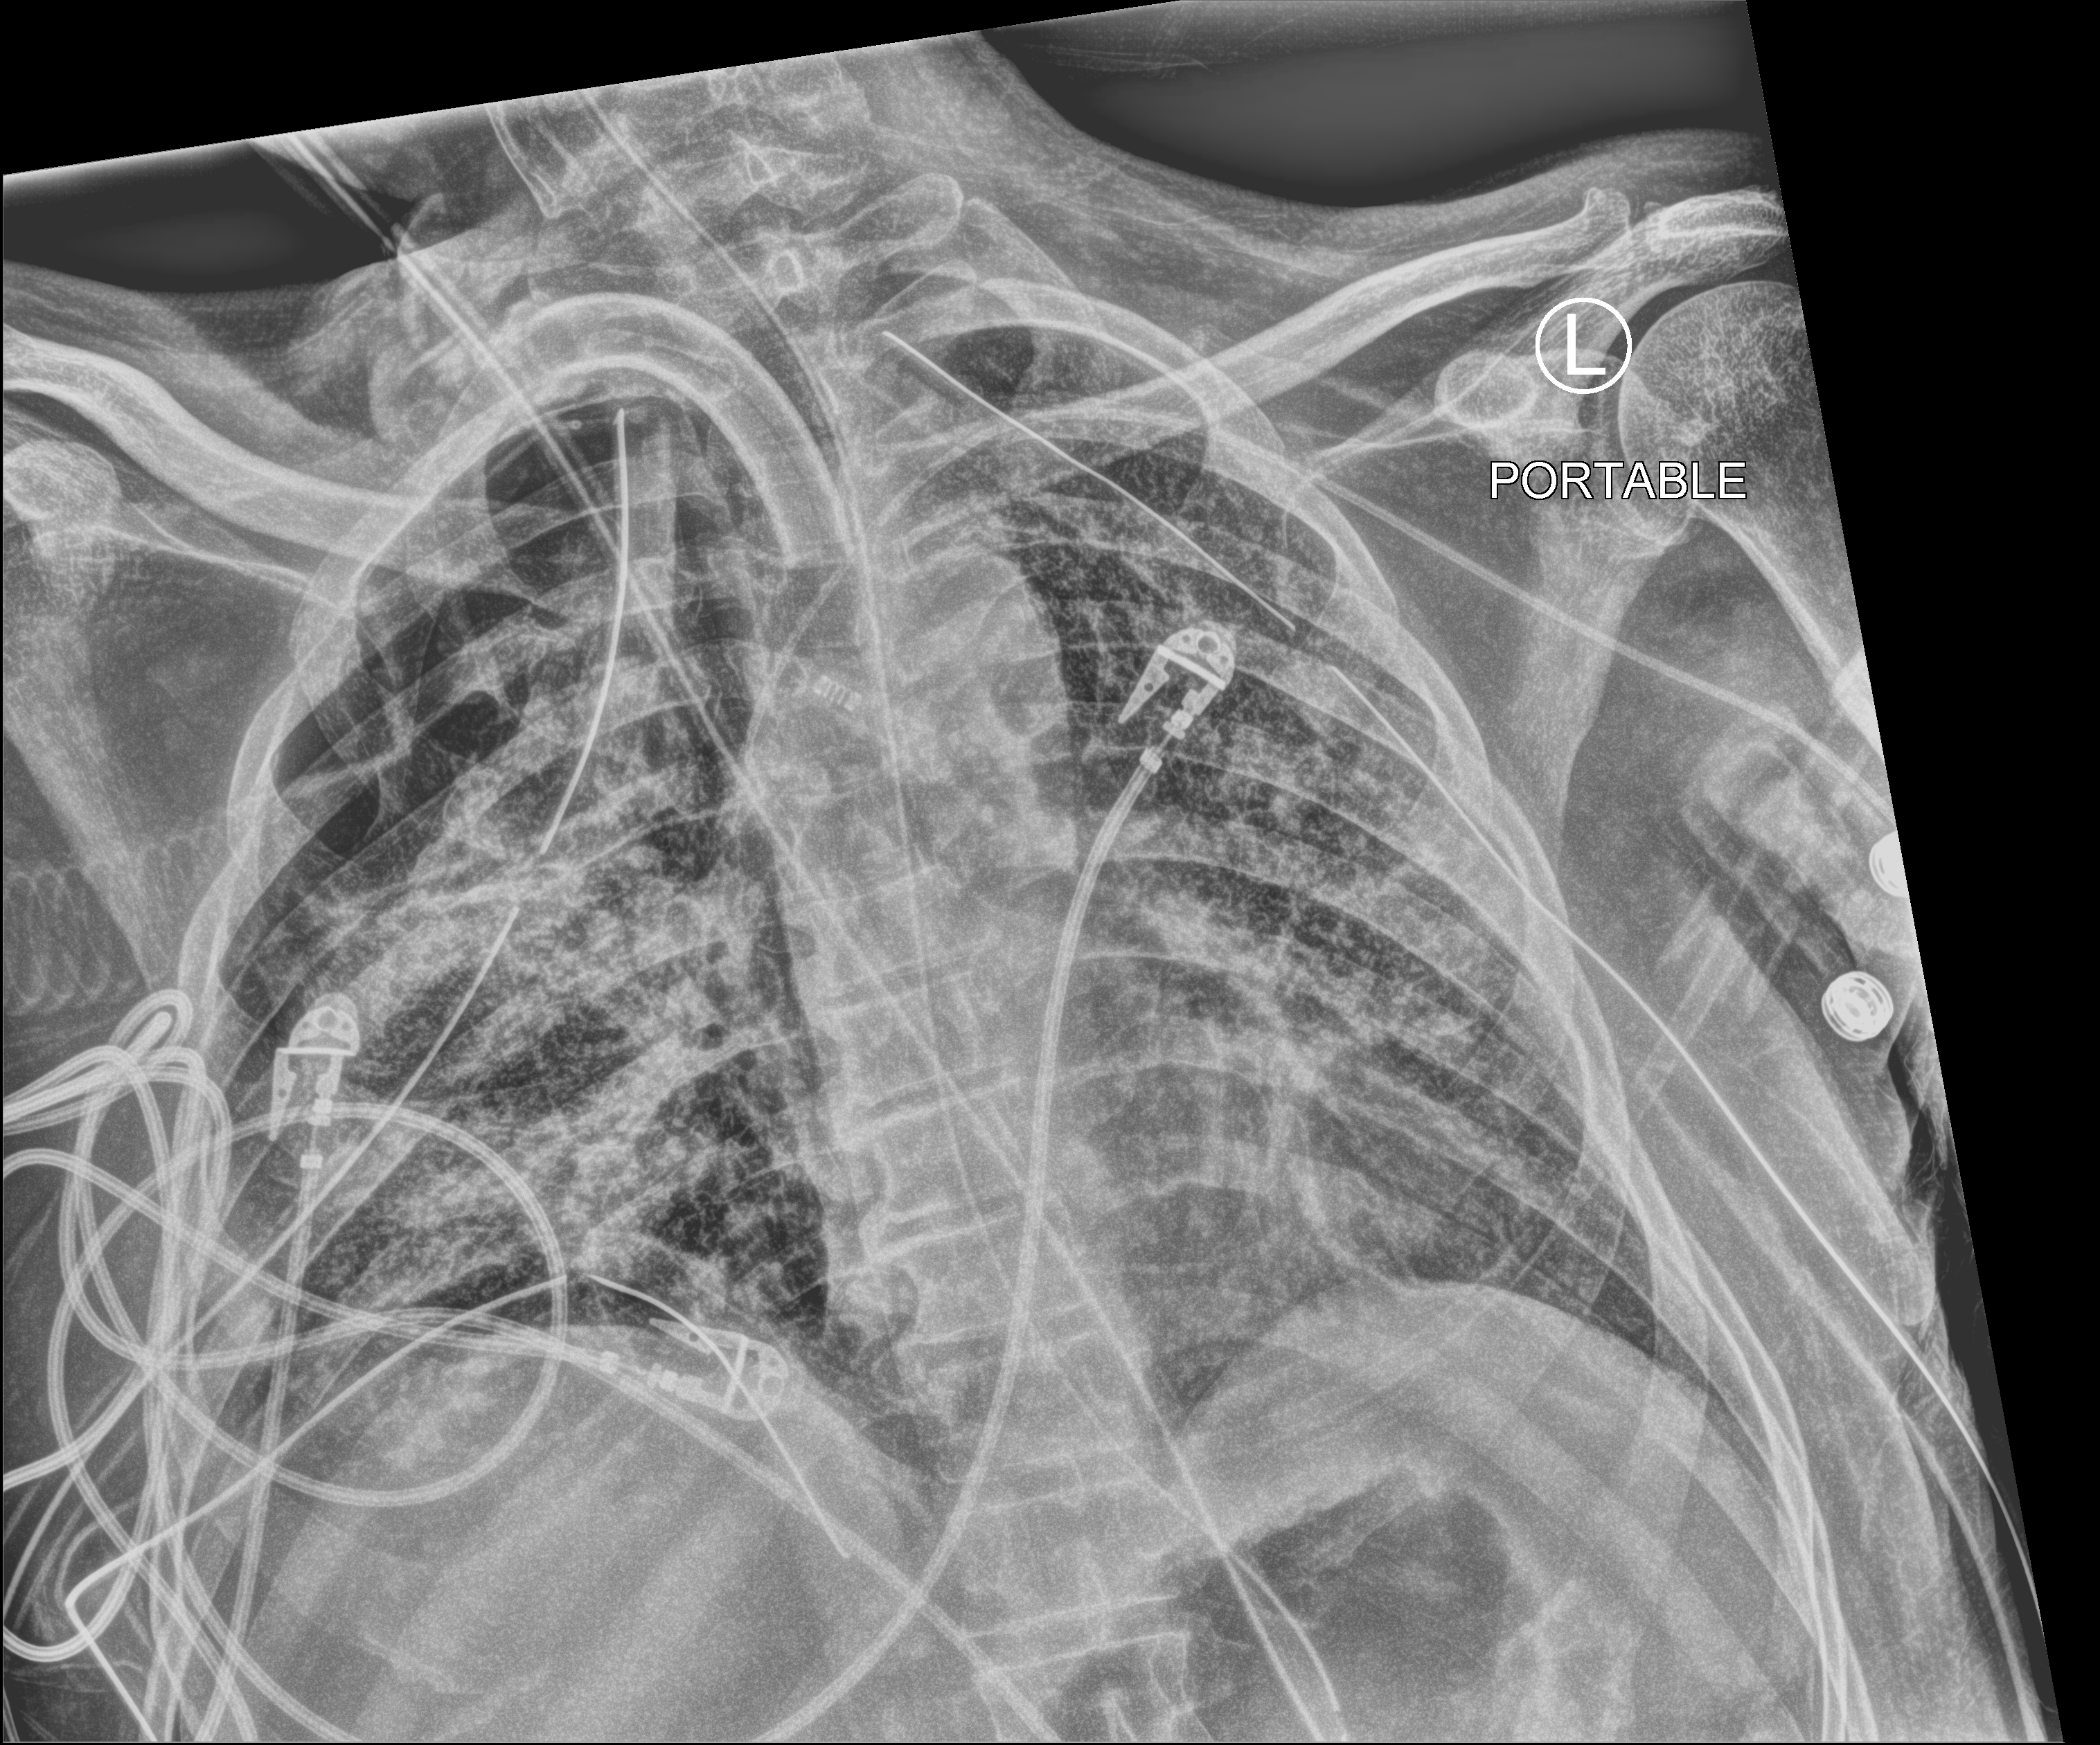
Portable chest radiograph; anteroposterior (AP) projection. Male patient hospitalised with COVID-19, age 18–59 years.
From the hospital-stay record, not from the radiograph (when in the stay this image was taken is not recorded): chronic kidney disease (admission record): no; admitted to intensive care during this hospital stay: yes; other chronic lung disease (admission record): no.